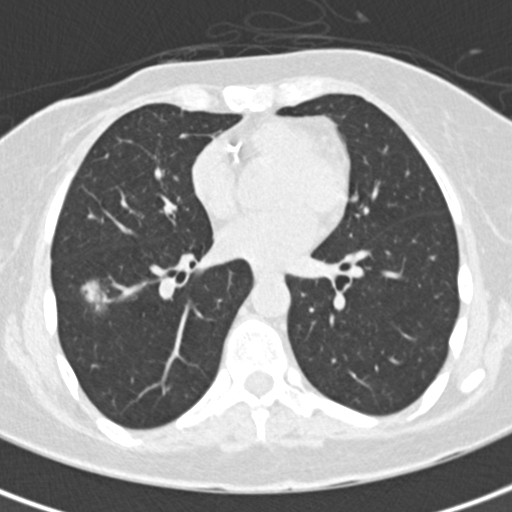
Low-dose screening chest CT, one axial slice; position 79 of 171 along the scan axis; 120 kVp; lung window (W 1500 / L -600 HU); 2 mm slice thickness; 512 × 512 image matrix, field of view 284 × 284 mm.
Outlined on this slice (manually delineated by an expert):
- lesion 1 (tumor, lower lobe of right lung): box from (x=81, y=280) to (x=108, y=312) px